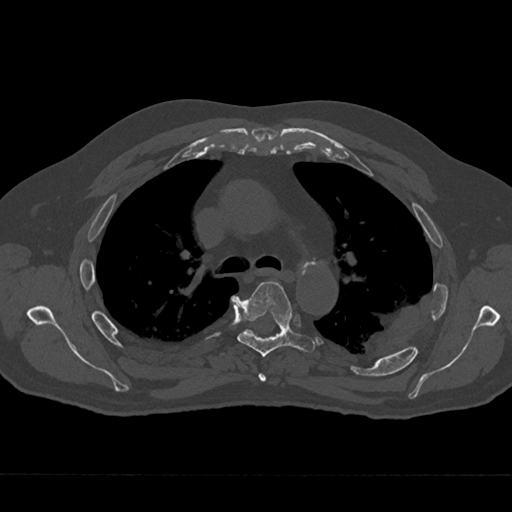
CT including the spine, one axial slice; slice 474 of 797 in the series (ordered by position); reconstruction kernel Br40s/3; 120 kVp; bone window (W 1800 / L 400 HU); 0.5 mm slice thickness; 512 × 512 image matrix, field of view 377 × 377 mm. Male patient, age 75 years. From the clinical record (not read from this slice): primary cancer: renal; vertebrae with lytic lesions (as recorded): T4.
Structures marked on this image (semi-automatic segmentation, software-assisted and operator-edited):
- T4 vertebra: bounding box [x1, y1, x2, y2] px = [258, 373, 266, 382]
- T5 vertebra: [236, 281, 315, 357]
- T6 vertebra: [246, 330, 252, 333]